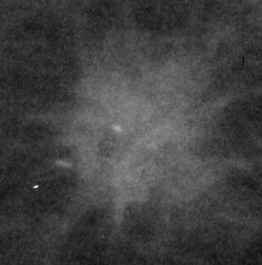
Crop from a digitized film mammogram around one marked abnormality; right breast; CC view.
- Marked abnormality: mass, shape irregular, margins spiculated; BI-RADS assessment category 5; pathology (as recorded): malignant.